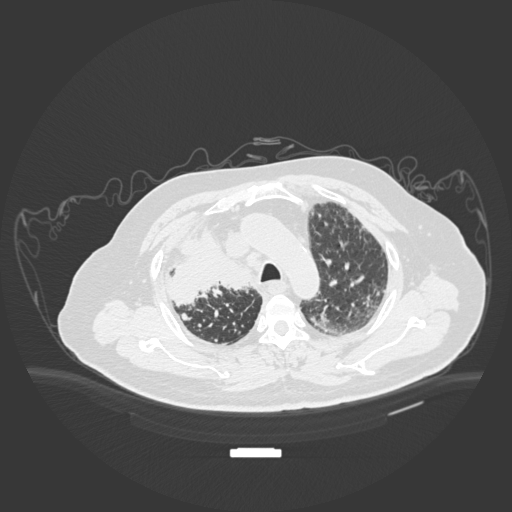
Chest CT, one axial slice. Position 141 of 201 along the scan axis. Reconstruction kernel B30f. 120 kVp. Lung window (W 1500 / L -600 HU). 1 mm slice thickness. 512 × 512 image matrix, field of view 500 × 500 mm. Male patient, age 69 years. From the clinical record (not read from this slice): clinical TNM (as recorded): T4 N3 M1.
Outlined on this slice (rectangle marked by the reading radiologist):
- lung tumour (recorded histology: adenocarcinoma): bounding box [x1, y1, x2, y2] px = [163, 227, 257, 314]